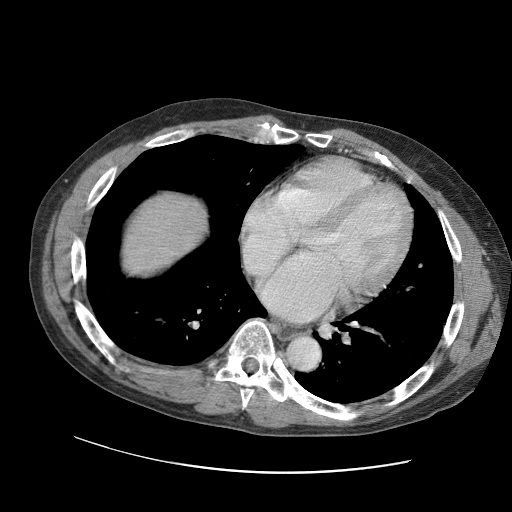
Contrast-enhanced abdominal CT (liver protocol), one axial slice; position 98 of 109 along the scan axis; 120 kVp; soft-tissue window (W 400 / L 40 HU); 2.5 mm slice thickness; 512 × 512 image matrix, field of view 400 × 400 mm. Case-level facts recorded for this patient, not image findings: diagnosis: hepatocellular carcinoma (patient treated with transarterial chemoembolisation; whether this scan precedes or follows treatment is not stated here); TNM stage (as recorded): Stage-IIIC; Child-Pugh class: B; tumour differentiation: well differentiated.
Annotated regions visible in this slice (semi-automatically segmented with operator editing):
- liver parenchyma outside the tumour (the mass and vessels are separate outlines, so this box may not span the whole liver): box from (x=120, y=192) to (x=206, y=272) px